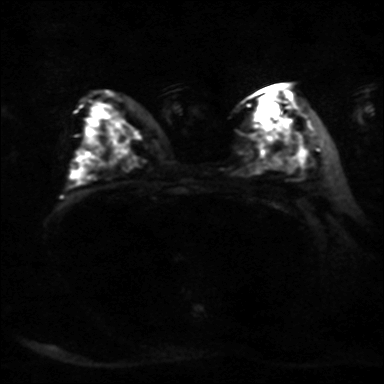
Breast MRI, one axial slice; position 21 of 36 along the scan axis; diffusion-weighted series; image 2 of 4 stored at this slice position (different b-values; order by instance number); 3 T; 384 × 384 image matrix, field of view 320 × 320 mm. Female patient.
Annotated regions visible in this slice (manually delineated by an expert):
- tumour on diffusion-weighted imaging: bounding box [x1, y1, x2, y2] px = [282, 115, 291, 125]